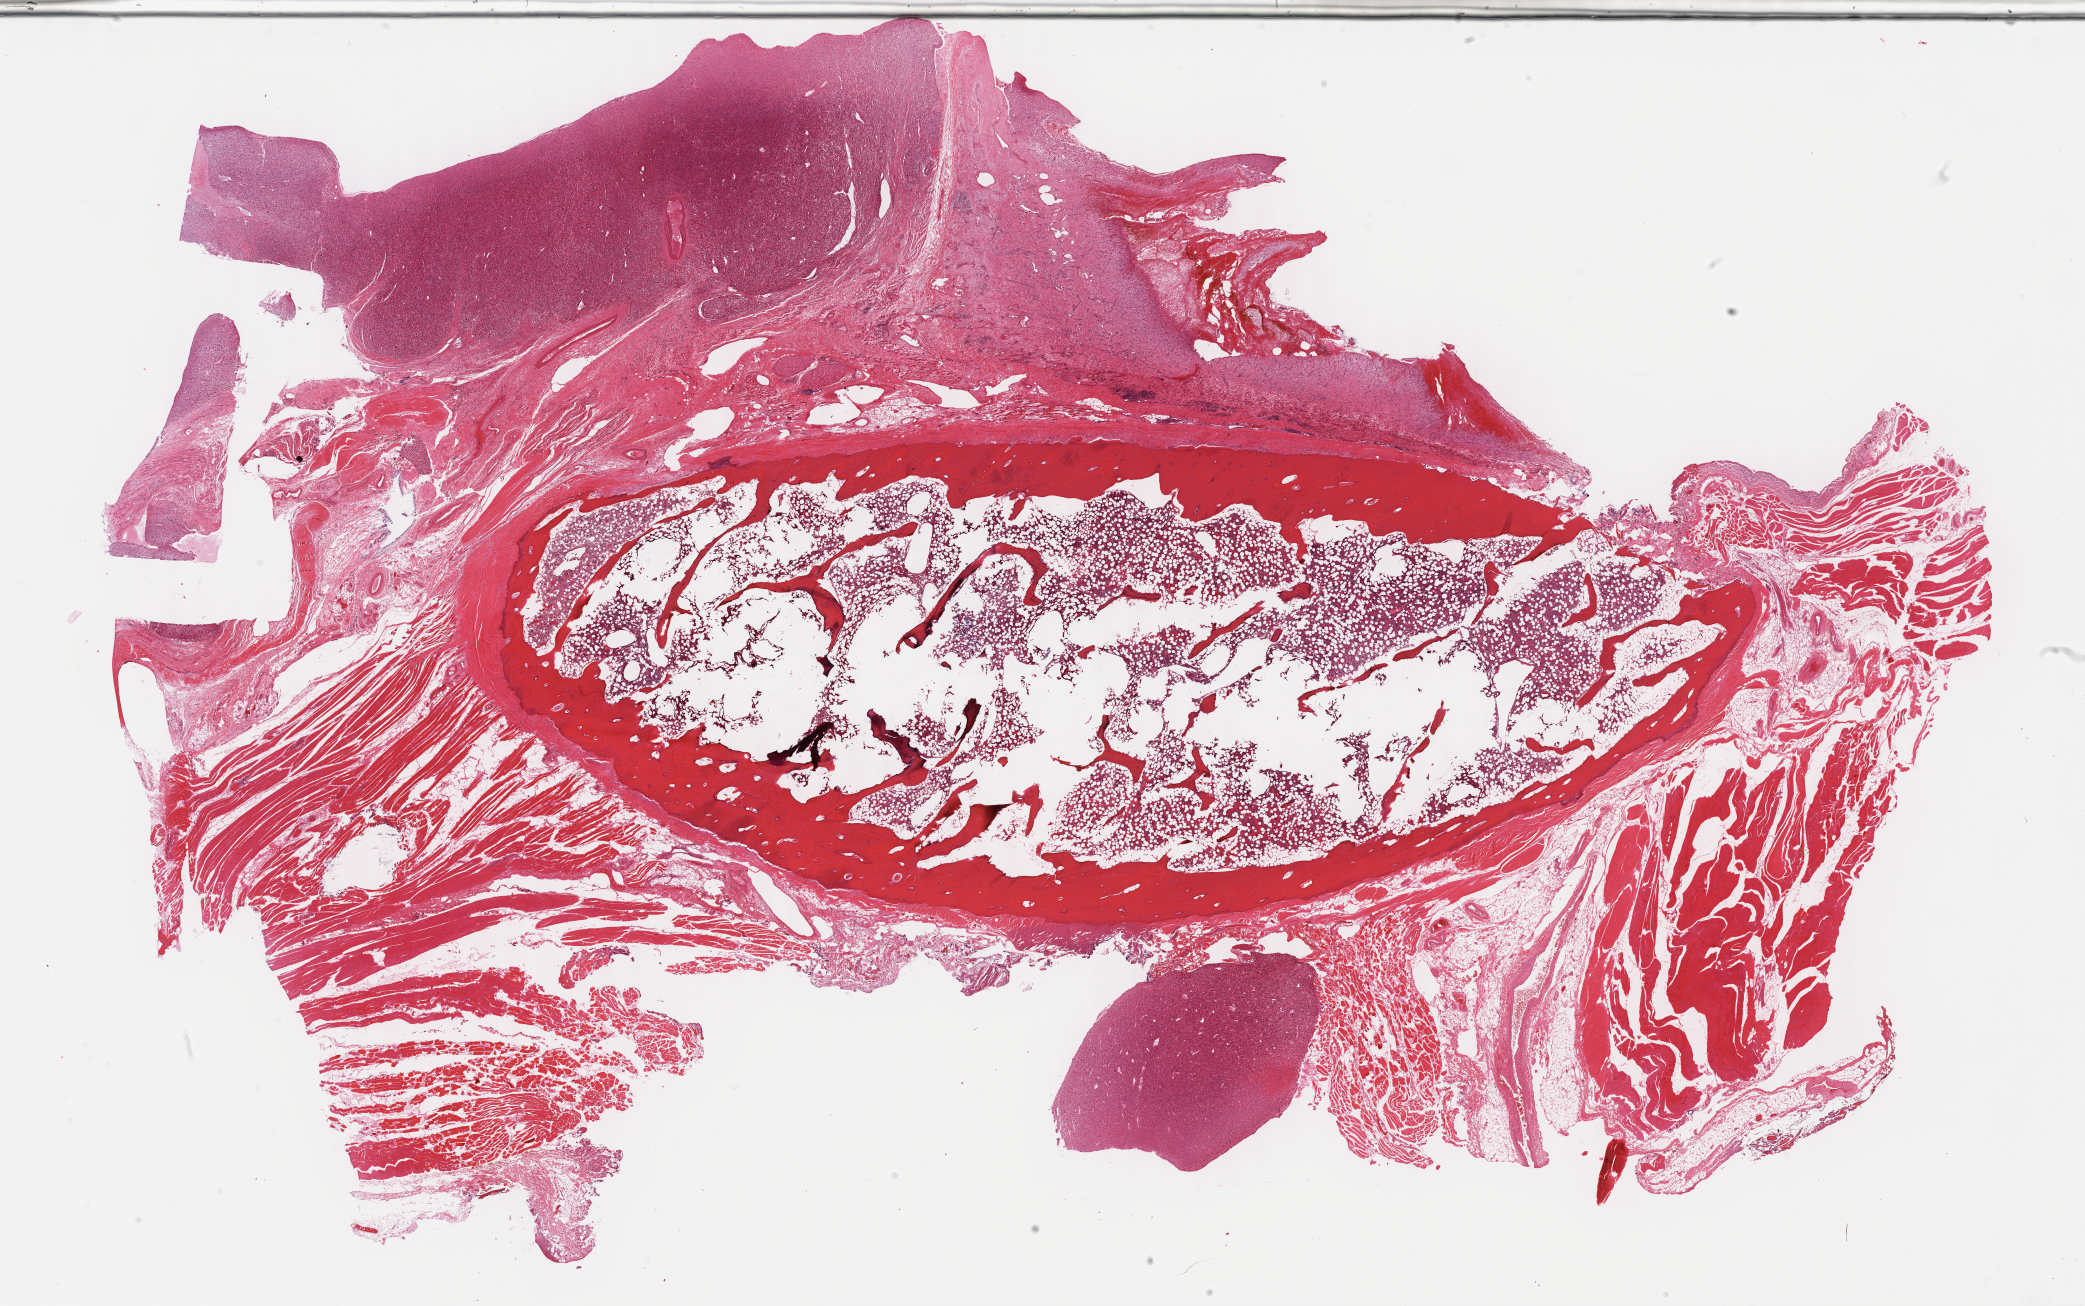
Whole-slide histology image, H&E, whole scanned area (about 33.7 x 21.1 mm, from a 40x scan) shown as a low-resolution overview. FFPE section. Primary tumour sample from the connective, subcutaneous and other soft tissues. Patient: female, age at initial diagnosis 49 years.
Histologic diagnosis: Undifferentiated sarcoma.